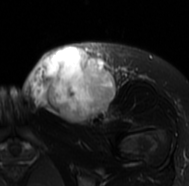
MRI of an extremity soft-tissue mass, one axial slice. Position 39 of 77 along the scan axis. T2-weighted fat-saturated. MR volume resampled by the dataset authors to the PET/CT grid (not the native acquisition matrix). 3.27 mm slice thickness. 189 × 186 image matrix, field of view 185 × 182 mm. Female patient. From the clinical record (not read from this slice): histological type: leiomyosarcoma; grade: high; site of the primary tumour: groin.
Annotated regions visible in this slice (expert contour drawn on MRI and transferred to this co-registered scan by the dataset authors):
- gross tumour volume including surrounding oedema: bounding box (x1, y1, x2, y2) in pixels: (22, 40, 135, 126)
- gross tumour volume (mass): (31, 45, 116, 123)